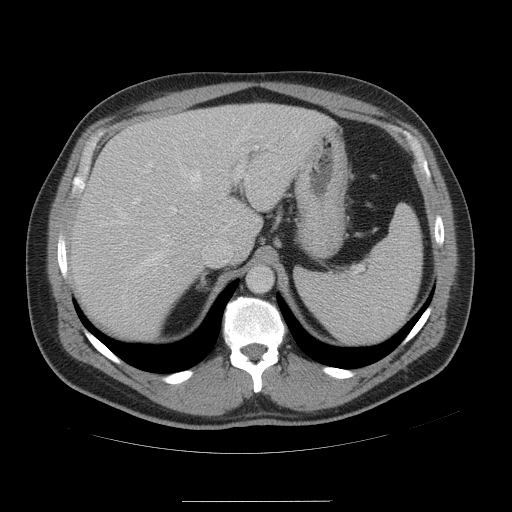
Contrast-enhanced abdominal CT, one axial slice; position 37 of 54 along the scan axis; intravenous contrast given; soft-tissue window (W 400 / L 40 HU); 512 × 512 image matrix. Male patient, age 40 years. Case-level facts recorded for this patient, not image findings: diagnosis: colorectal cancer liver metastases, imaged before liver resection; multiple liver metastases: no; largest metastasis: 15 cm; disease in both lobes: no.
Structures marked on this image (manually delineated by an expert):
- hepatic veins: bounding box [x1, y1, x2, y2] px = [119, 153, 231, 276]
- liver: [70, 103, 335, 340]
- planned liver remnant (the part of the liver to remain after resection): [182, 103, 334, 270]
- portal vein (with intrahepatic branches): [137, 134, 246, 213]